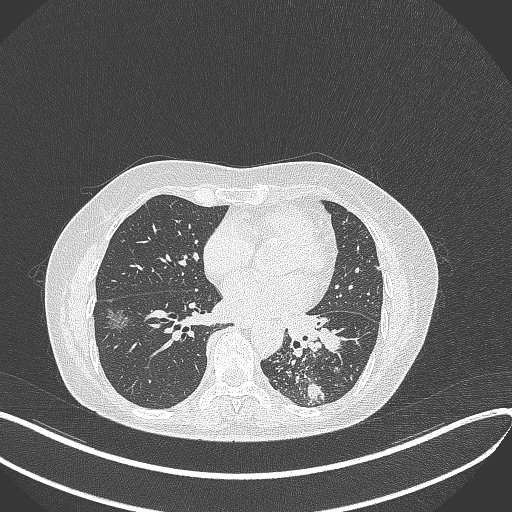
Chest CT, one axial slice. Slice 174 of 429 in the series (ordered by position). Reconstruction kernel B70f. 100 kVp. Lung window (W 1500 / L -600 HU). 512 × 512 image matrix. Female patient, age 63 years. Case-level facts recorded for this patient, not image findings: clinical TNM (as recorded): T1b N0 M0.
Structures marked on this image (bounding box drawn by a radiologist):
- lung tumour (recorded histology: adenocarcinoma): box from (x=283, y=306) to (x=348, y=363) px